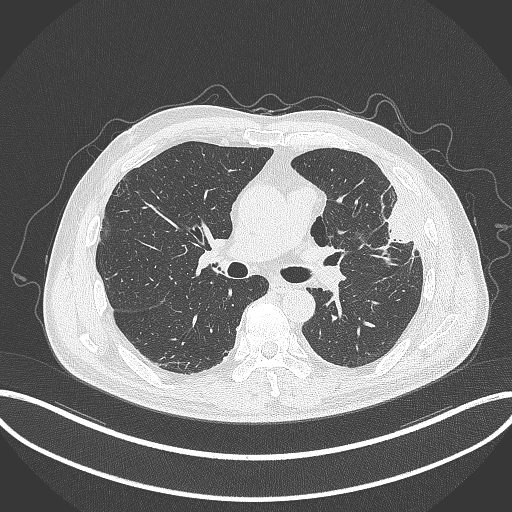
Chest CT, one axial slice; position 194 of 382 along the scan axis; reconstruction kernel B70f; 120 kVp; lung window (W 1500 / L -600 HU); 1 mm slice thickness; 512 × 512 image matrix, field of view 415 × 415 mm. Male patient, age 64 years. From the clinical record (not read from this slice): clinical TNM (as recorded): T4 N1 M0; histopathological grade: G3.
Structures marked on this image (rectangle marked by the reading radiologist):
- lung tumour (recorded histology: adenocarcinoma): bounding box [x1, y1, x2, y2] px = [373, 183, 419, 259]